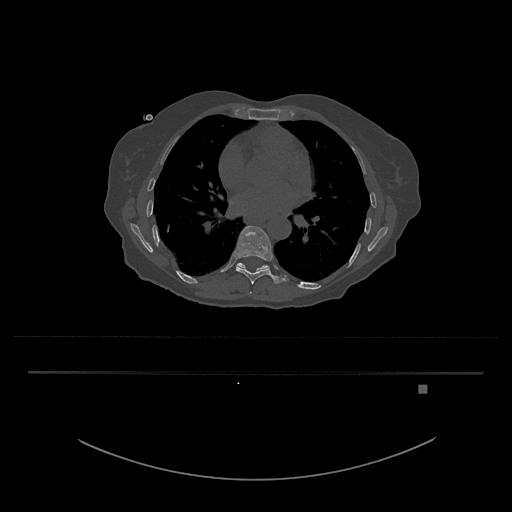
CT including the spine, one axial slice. Position 751 of 797 along the scan axis. Reconstruction kernel Br40s/3. 120 kVp. Bone window (W 1800 / L 400 HU). 0.5 mm slice thickness. 512 × 512 image matrix, field of view 500 × 500 mm. Patient: female, 57 years. Case-level facts recorded for this patient, not image findings: primary cancer: cervical.
Structures marked on this image (semi-automatically segmented with operator editing):
- T10 vertebra: bounding box (x1, y1, x2, y2) in pixels: (236, 262, 270, 272)
- T8 vertebra: (250, 291, 252, 294)
- T9 vertebra: (235, 225, 284, 285)